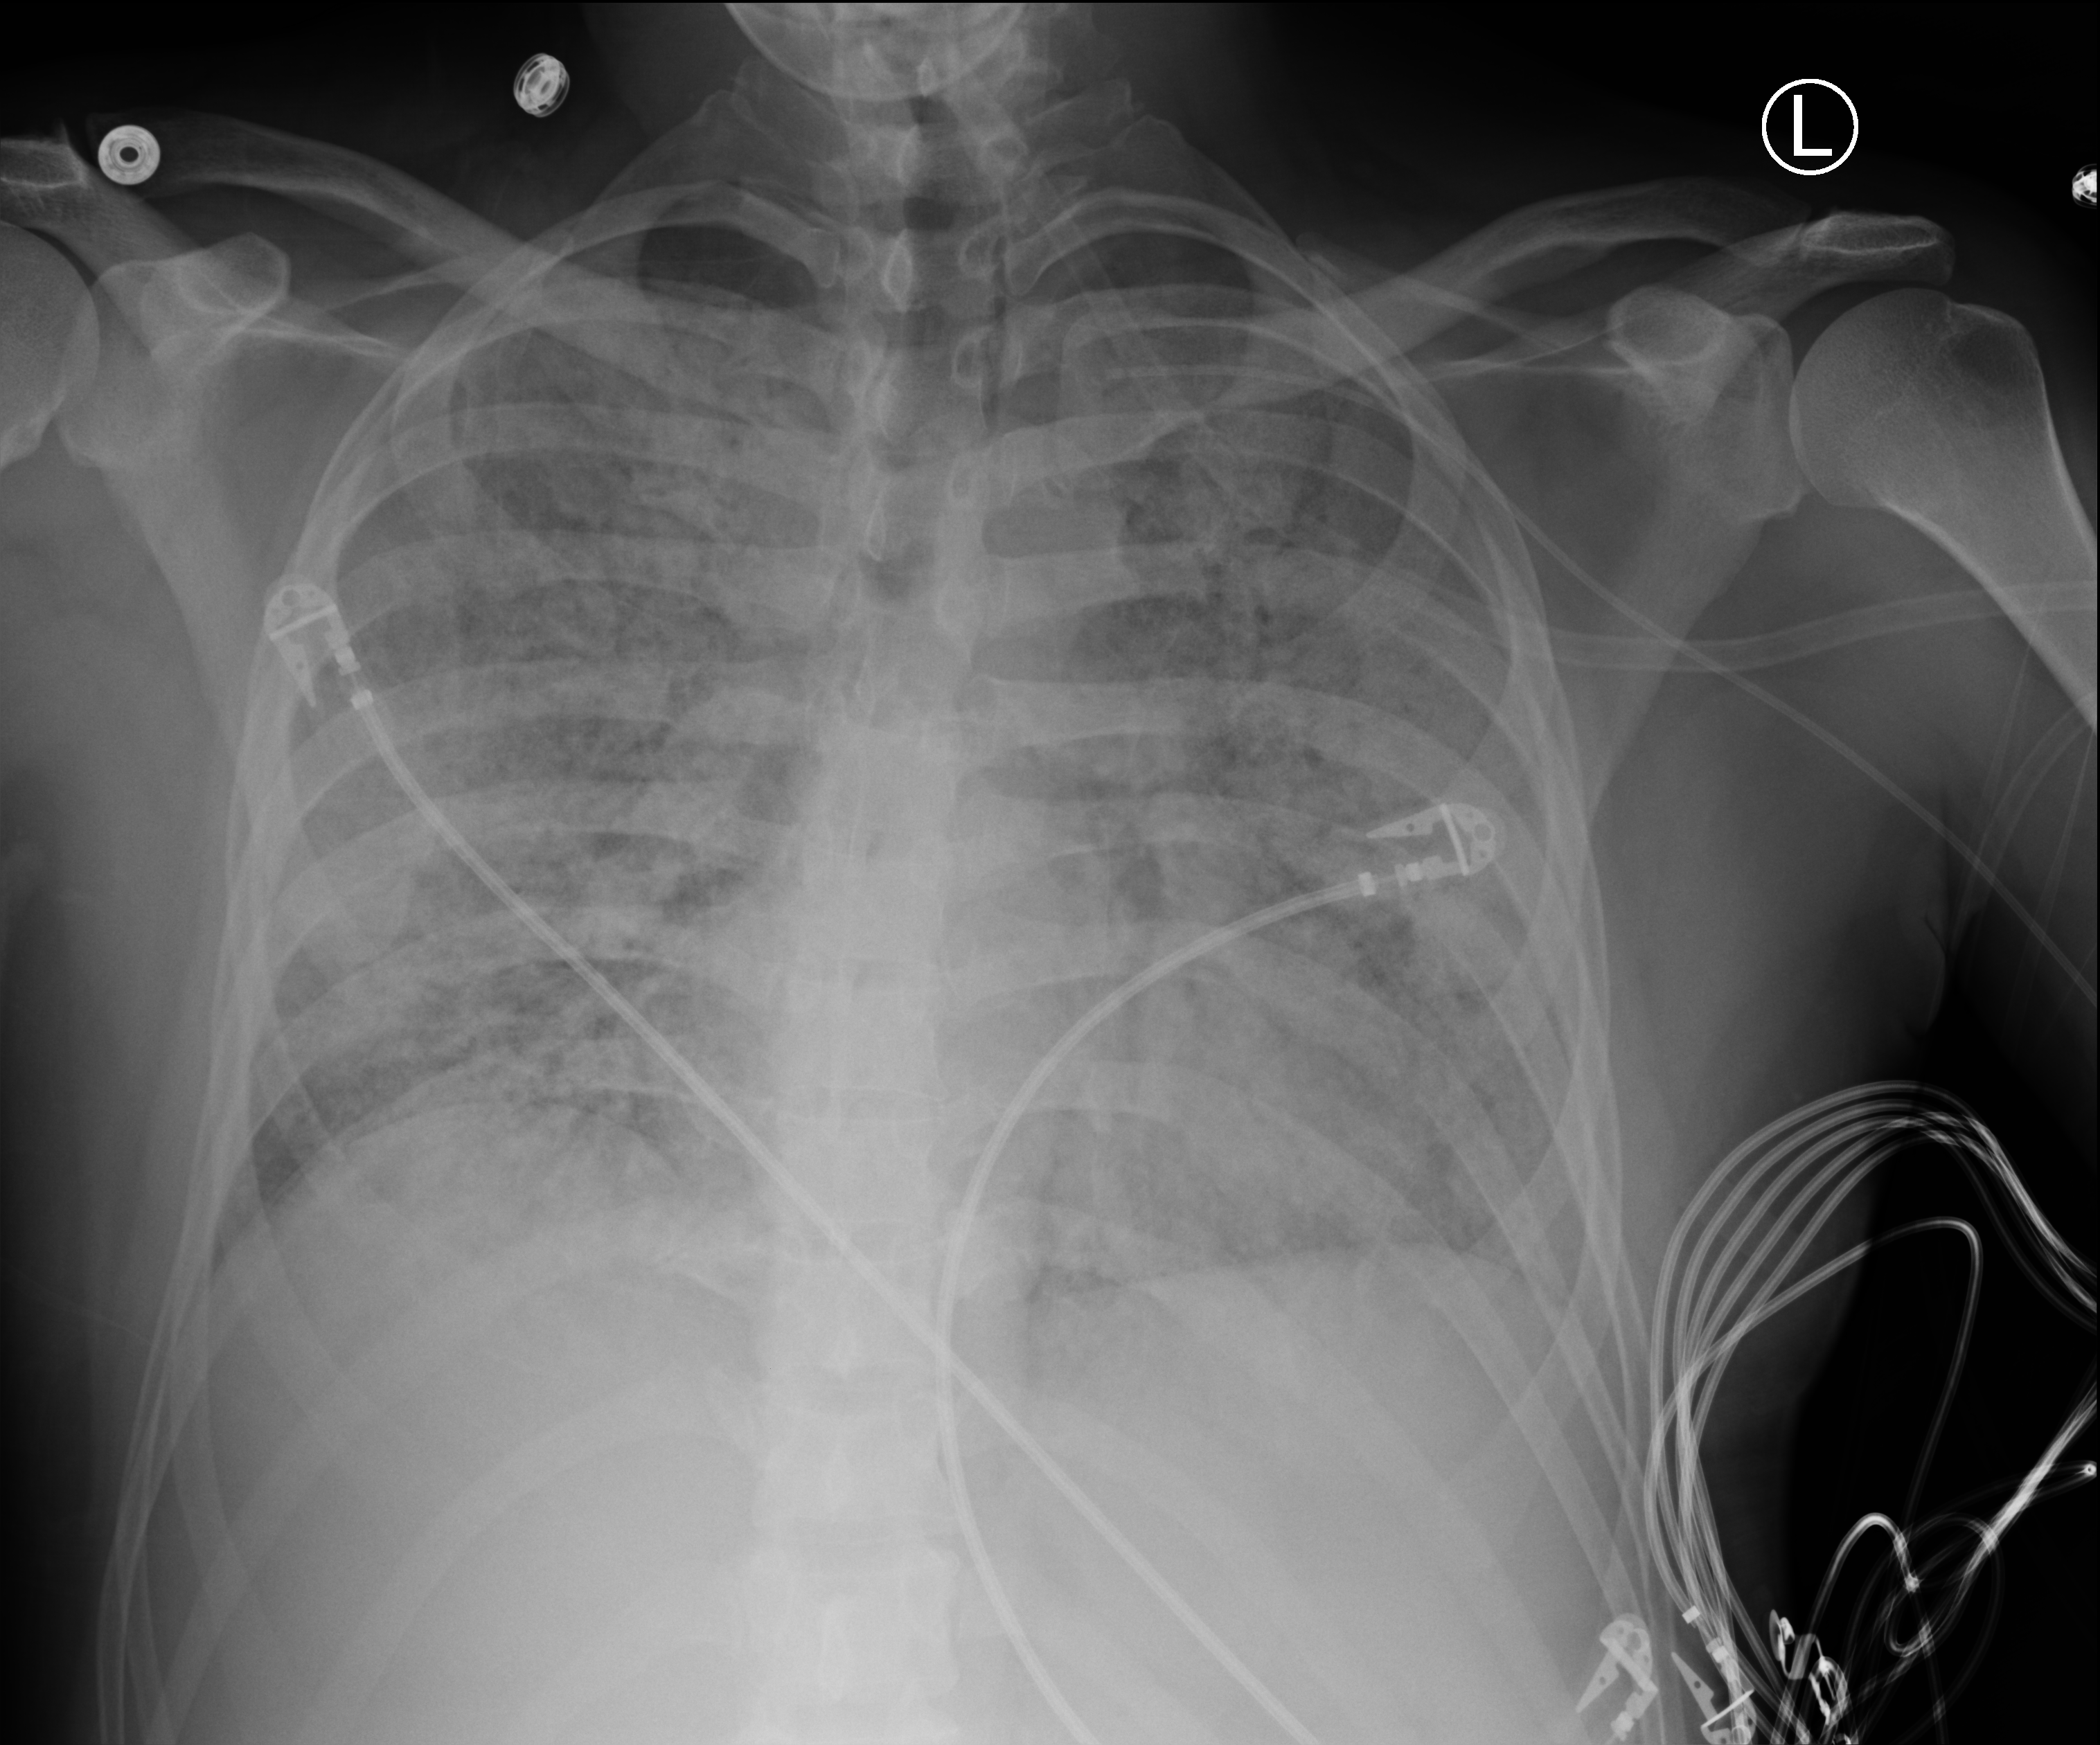
Chest X-ray (portable). Patient hospitalised with COVID-19; male, aged 18–59 years.
From the hospital-stay record, not from the radiograph (when in the stay this image was taken is not recorded): admitted to intensive care during this hospital stay: yes; length of hospital stay: 30 days.